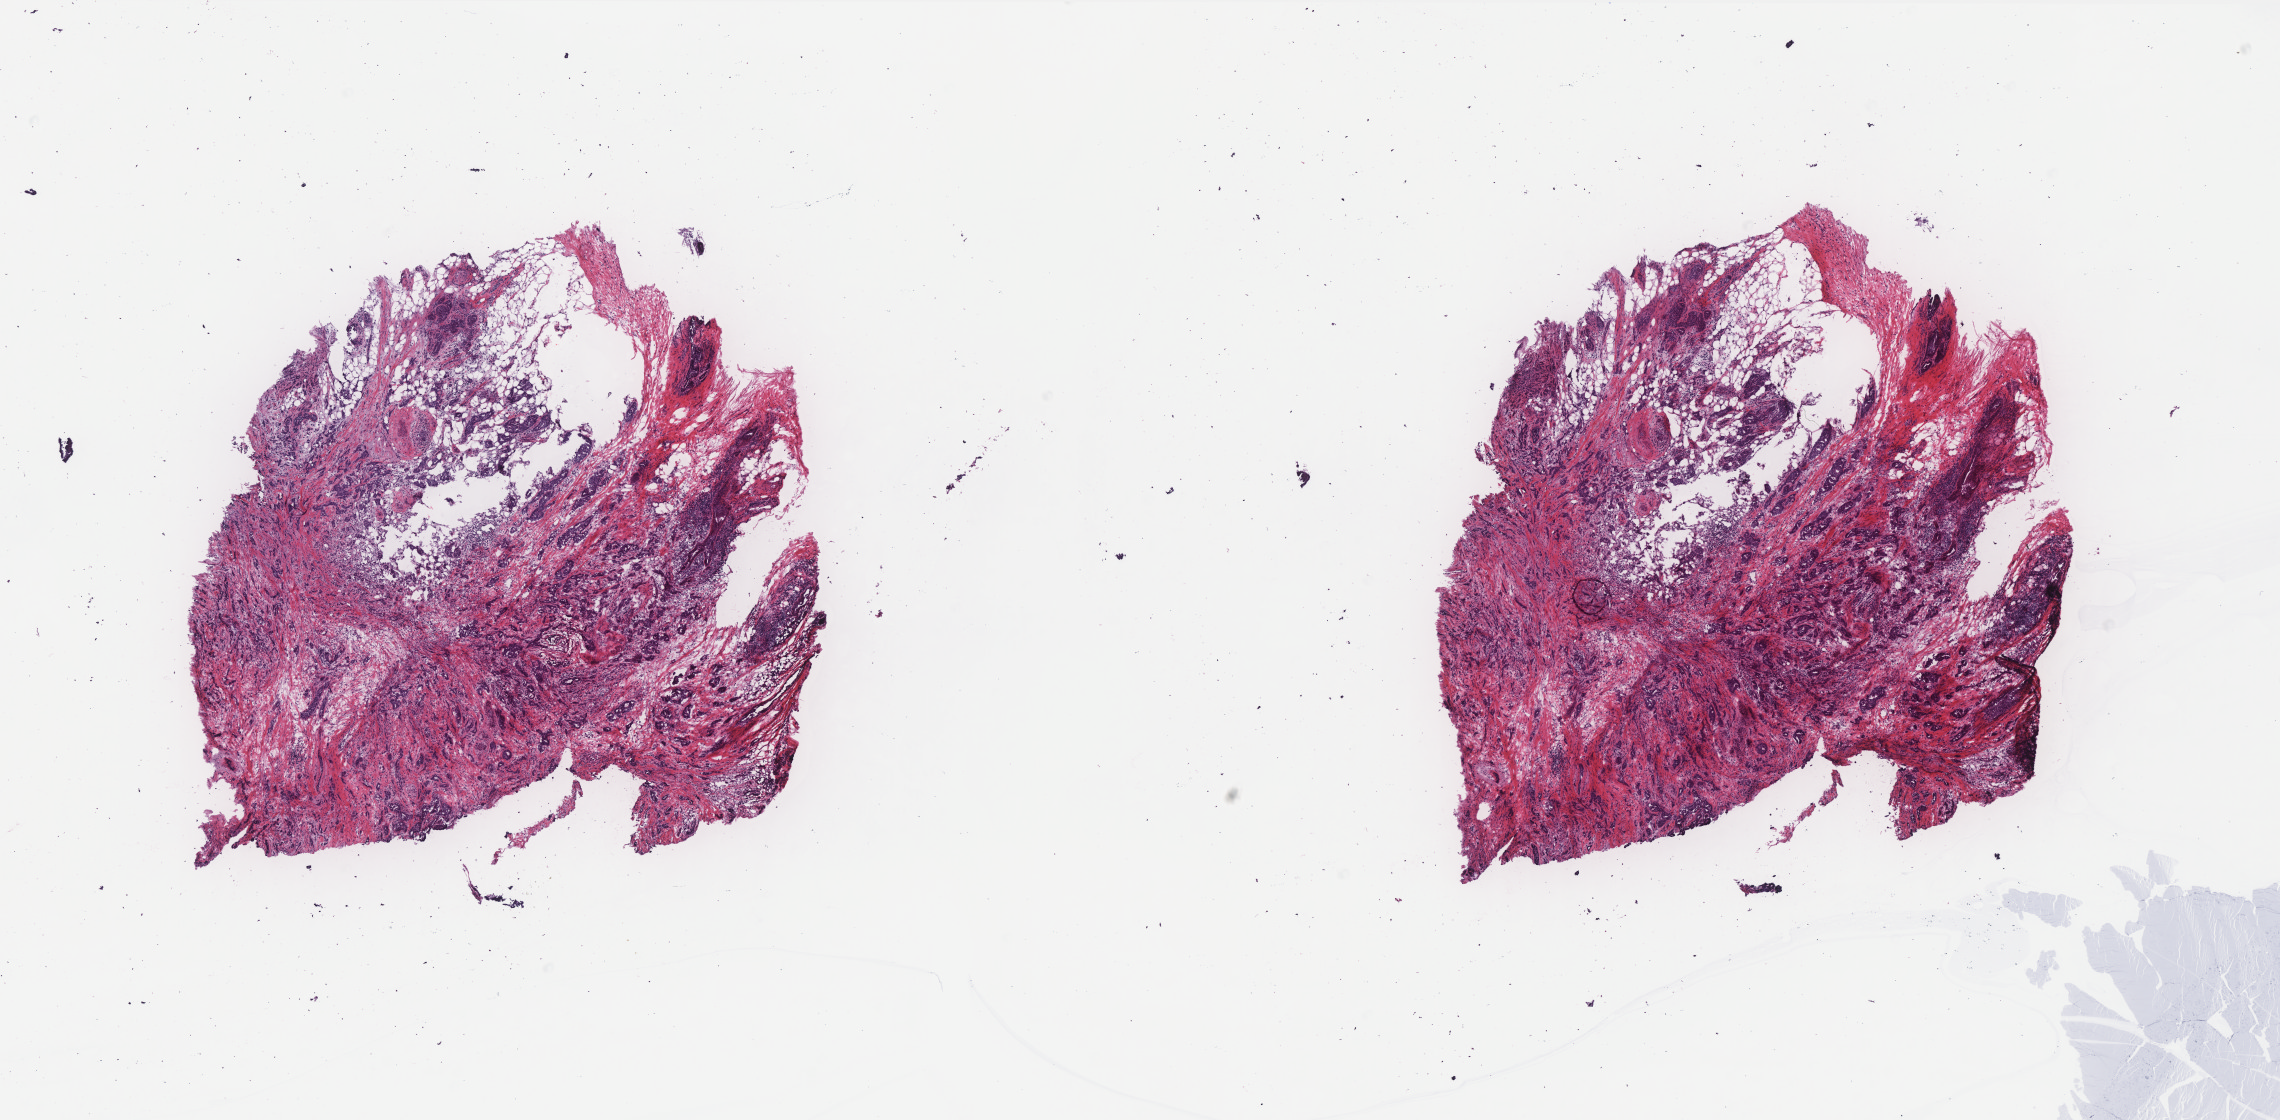
H&E whole-slide image, whole scanned area (about 18.3 x 9.0 mm, acquisition: 40x scan) shown as a low-resolution overview. Frozen section. Sample: primary tumour, breast. Female, age 47 years at initial diagnosis. Composition of this section per pathologist review: tumour cells 85%, tumour nuclei 55%, normal cells 5%, stromal cells 10%, necrosis 0%. Inflammatory infiltration, as recorded: lymphocyte infiltration 0%, monocyte infiltration 0%, neutrophil infiltration 0%.
Lymph nodes positive (case pathology): 0 of 27 examined. Laterality: right. Diagnosis: Infiltrating duct carcinoma, NOS. AJCC pathologic stage: IIA.